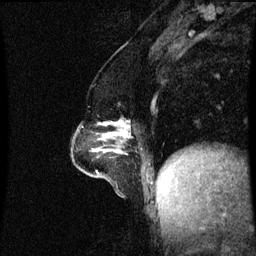
Breast MRI (dynamic contrast-enhanced), one sagittal slice; slice 24 of 60 in the series (ordered by position); dynamic contrast-enhanced series, image 2 of 3 at this slice position (ordered by acquisition); 1.5 T; TE 4.2 ms, TR 8.9 ms; 256 × 256 image matrix. Female patient, age 47 years. Case-level facts recorded for this patient, not image findings: setting: breast cancer imaged before/during neoadjuvant chemotherapy; receptor status: HR-positive, HER2-negative.
Annotated regions visible in this slice (semi-automatic segmentation, software-assisted and operator-edited):
- analysis volume of interest (the breast-tissue region the enhancement analysis was run in; not a lesion): bounding box (x1, y1, x2, y2) in pixels: (72, 122, 129, 161)
- tumour enhancement mask (voxels above the 70 % enhancement threshold inside the analysis volume of interest): (103, 122, 128, 137)